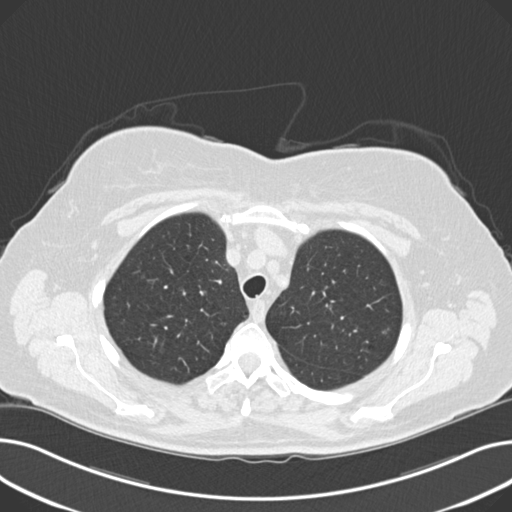
Low-dose screening chest CT, axial slice; third annual screen; lung window (W 1500 / L -600 HU); 120 kVp; slice 47 of 203 in the series; 512 × 512 image matrix. Female participant, aged 60 years at enrolment. Current smoker at enrolment.
Expert reader's lesion annotation, bounding box (x1, y1, x2, y2) in pixels: (371, 318, 403, 353). The screening reader recorded 8 non-calcified nodules or masses ≥4 mm on this exam; which of them this box marks is not recorded. Official screen result: positive, other. Lung cancer was diagnosed 176 days after this screen: non-small cell carcinoma, left upper lobe, poorly differentiated (G3), stage IB (AJCC 6th edition), 7 mm at pathology.